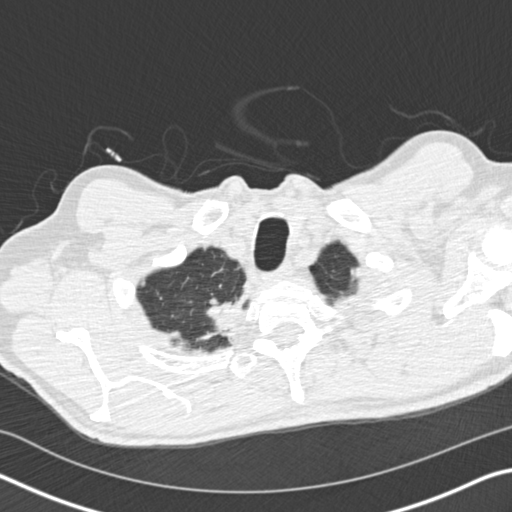
Low-dose screening chest CT, one axial slice. Position 160 of 175 along the scan axis. Reconstruction kernel B30f. 120 kVp. Lung window (W 1500 / L -600 HU). 2 mm slice thickness. 512 × 512 image matrix.
Annotated regions visible in this slice (expert manual segmentation):
- lesion 1 (tumor, upper lobe of right lung): bounding box [x1, y1, x2, y2] px = [205, 300, 249, 339]